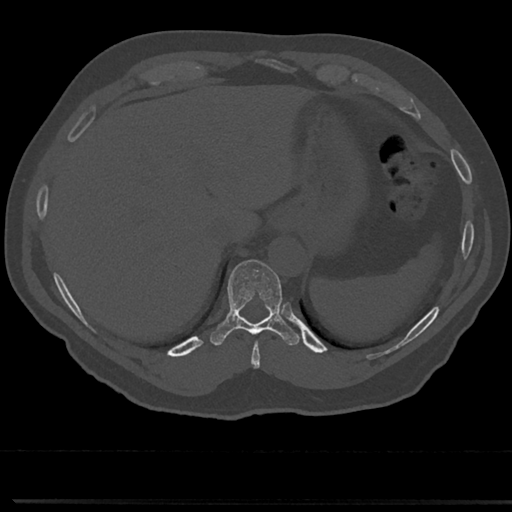
CT including the spine, one axial slice. Slice 261 of 817 in the series (ordered by position). 120 kVp. Bone window (W 1800 / L 400 HU). 0.5 mm slice thickness. 512 × 512 image matrix, field of view 355 × 355 mm. Male patient, age 61 years. Case-level facts recorded for this patient, not image findings: primary cancer: prostate.
Annotated regions visible in this slice (semi-automatic segmentation, software-assisted and operator-edited):
- T10 vertebra: bounding box [x1, y1, x2, y2] px = [213, 260, 298, 344]
- T9 vertebra: [250, 331, 264, 358]